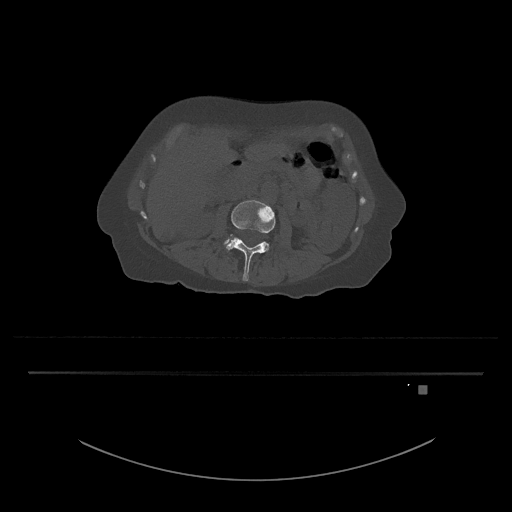
CT including the spine, one axial slice; slice 421 of 797 in the series (ordered by position); reconstruction kernel Br40s/3; bone window (W 1800 / L 400 HU); 0.5 mm slice thickness; 512 × 512 image matrix, field of view 500 × 500 mm. Female patient, age 57 years. From the clinical record (not read from this slice): primary cancer: cervical.
Structures marked on this image (semi-automatically segmented with operator editing):
- L3 vertebra: bounding box <224,200,276,281> (left, top, right, bottom; pixels)
- L4 vertebra: <224,240,229,244>